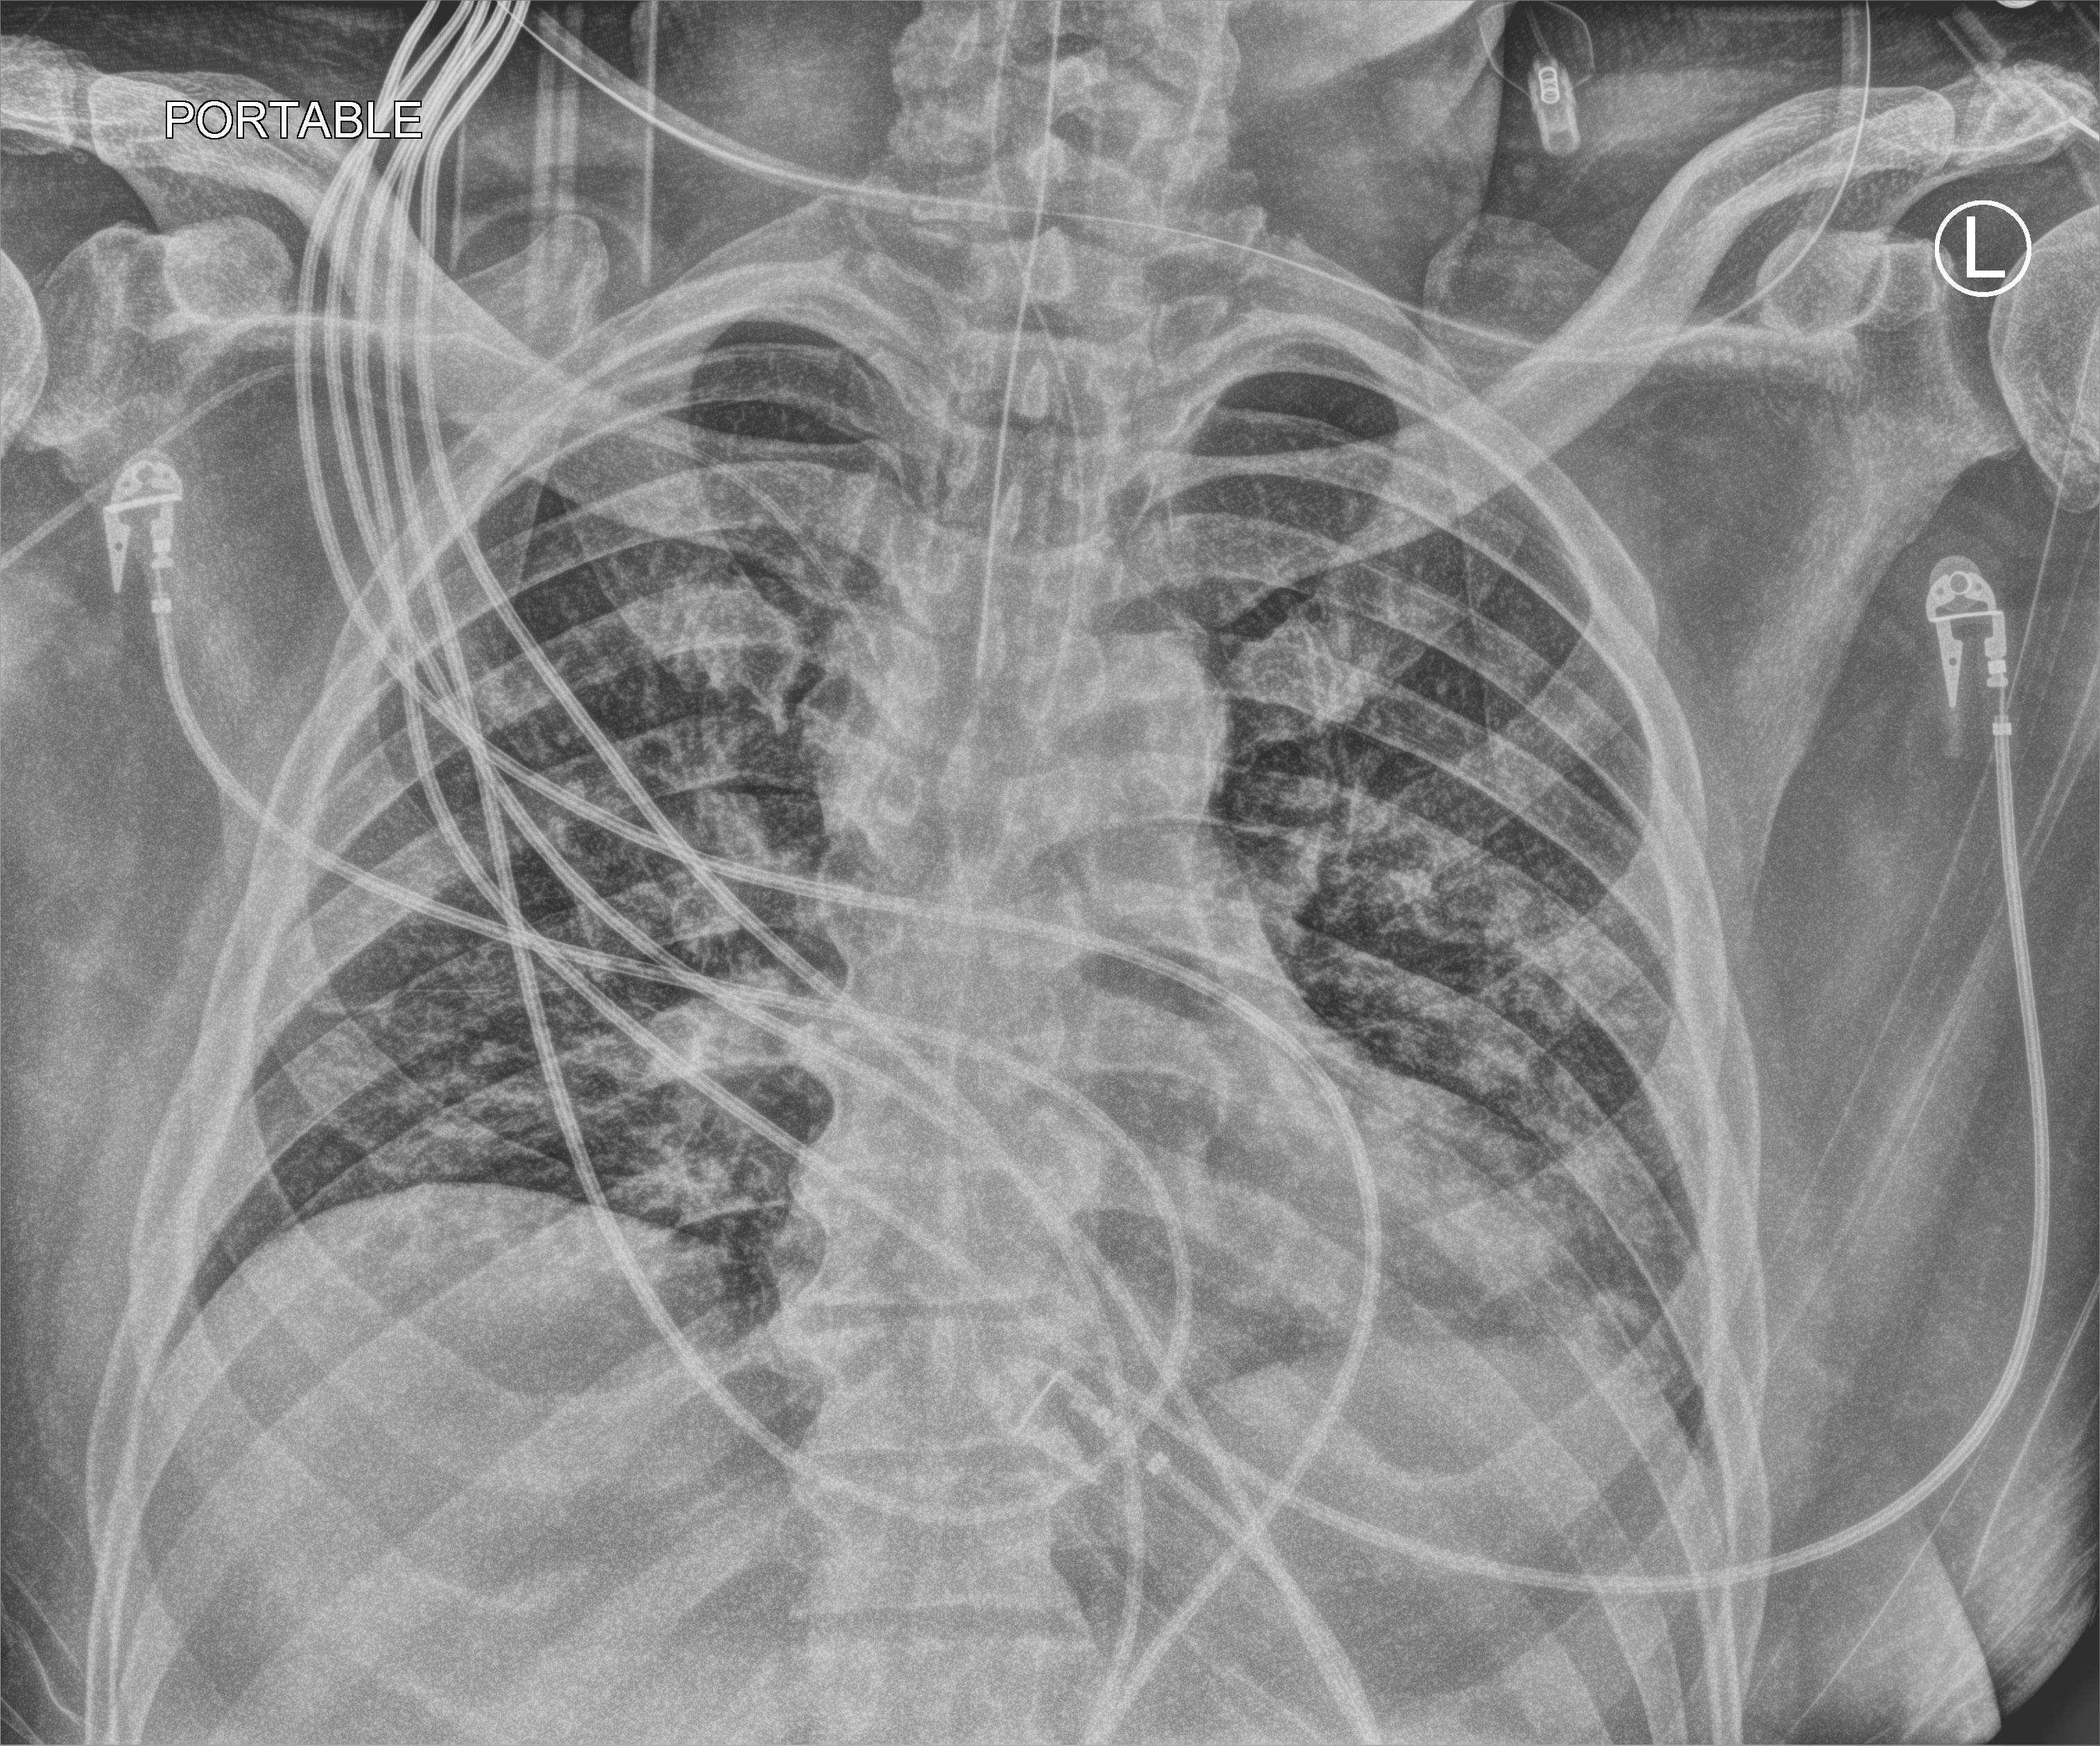
Bedside chest radiograph (computed radiography), anteroposterior (AP) projection. Patient hospitalised with COVID-19; male, aged 18–59 years.
Hospital-stay facts (about this admission, not read from this image; timing relative to this image not recorded):
- mechanically ventilated during this hospital stay: yes
- admitted to intensive care during this hospital stay: yes